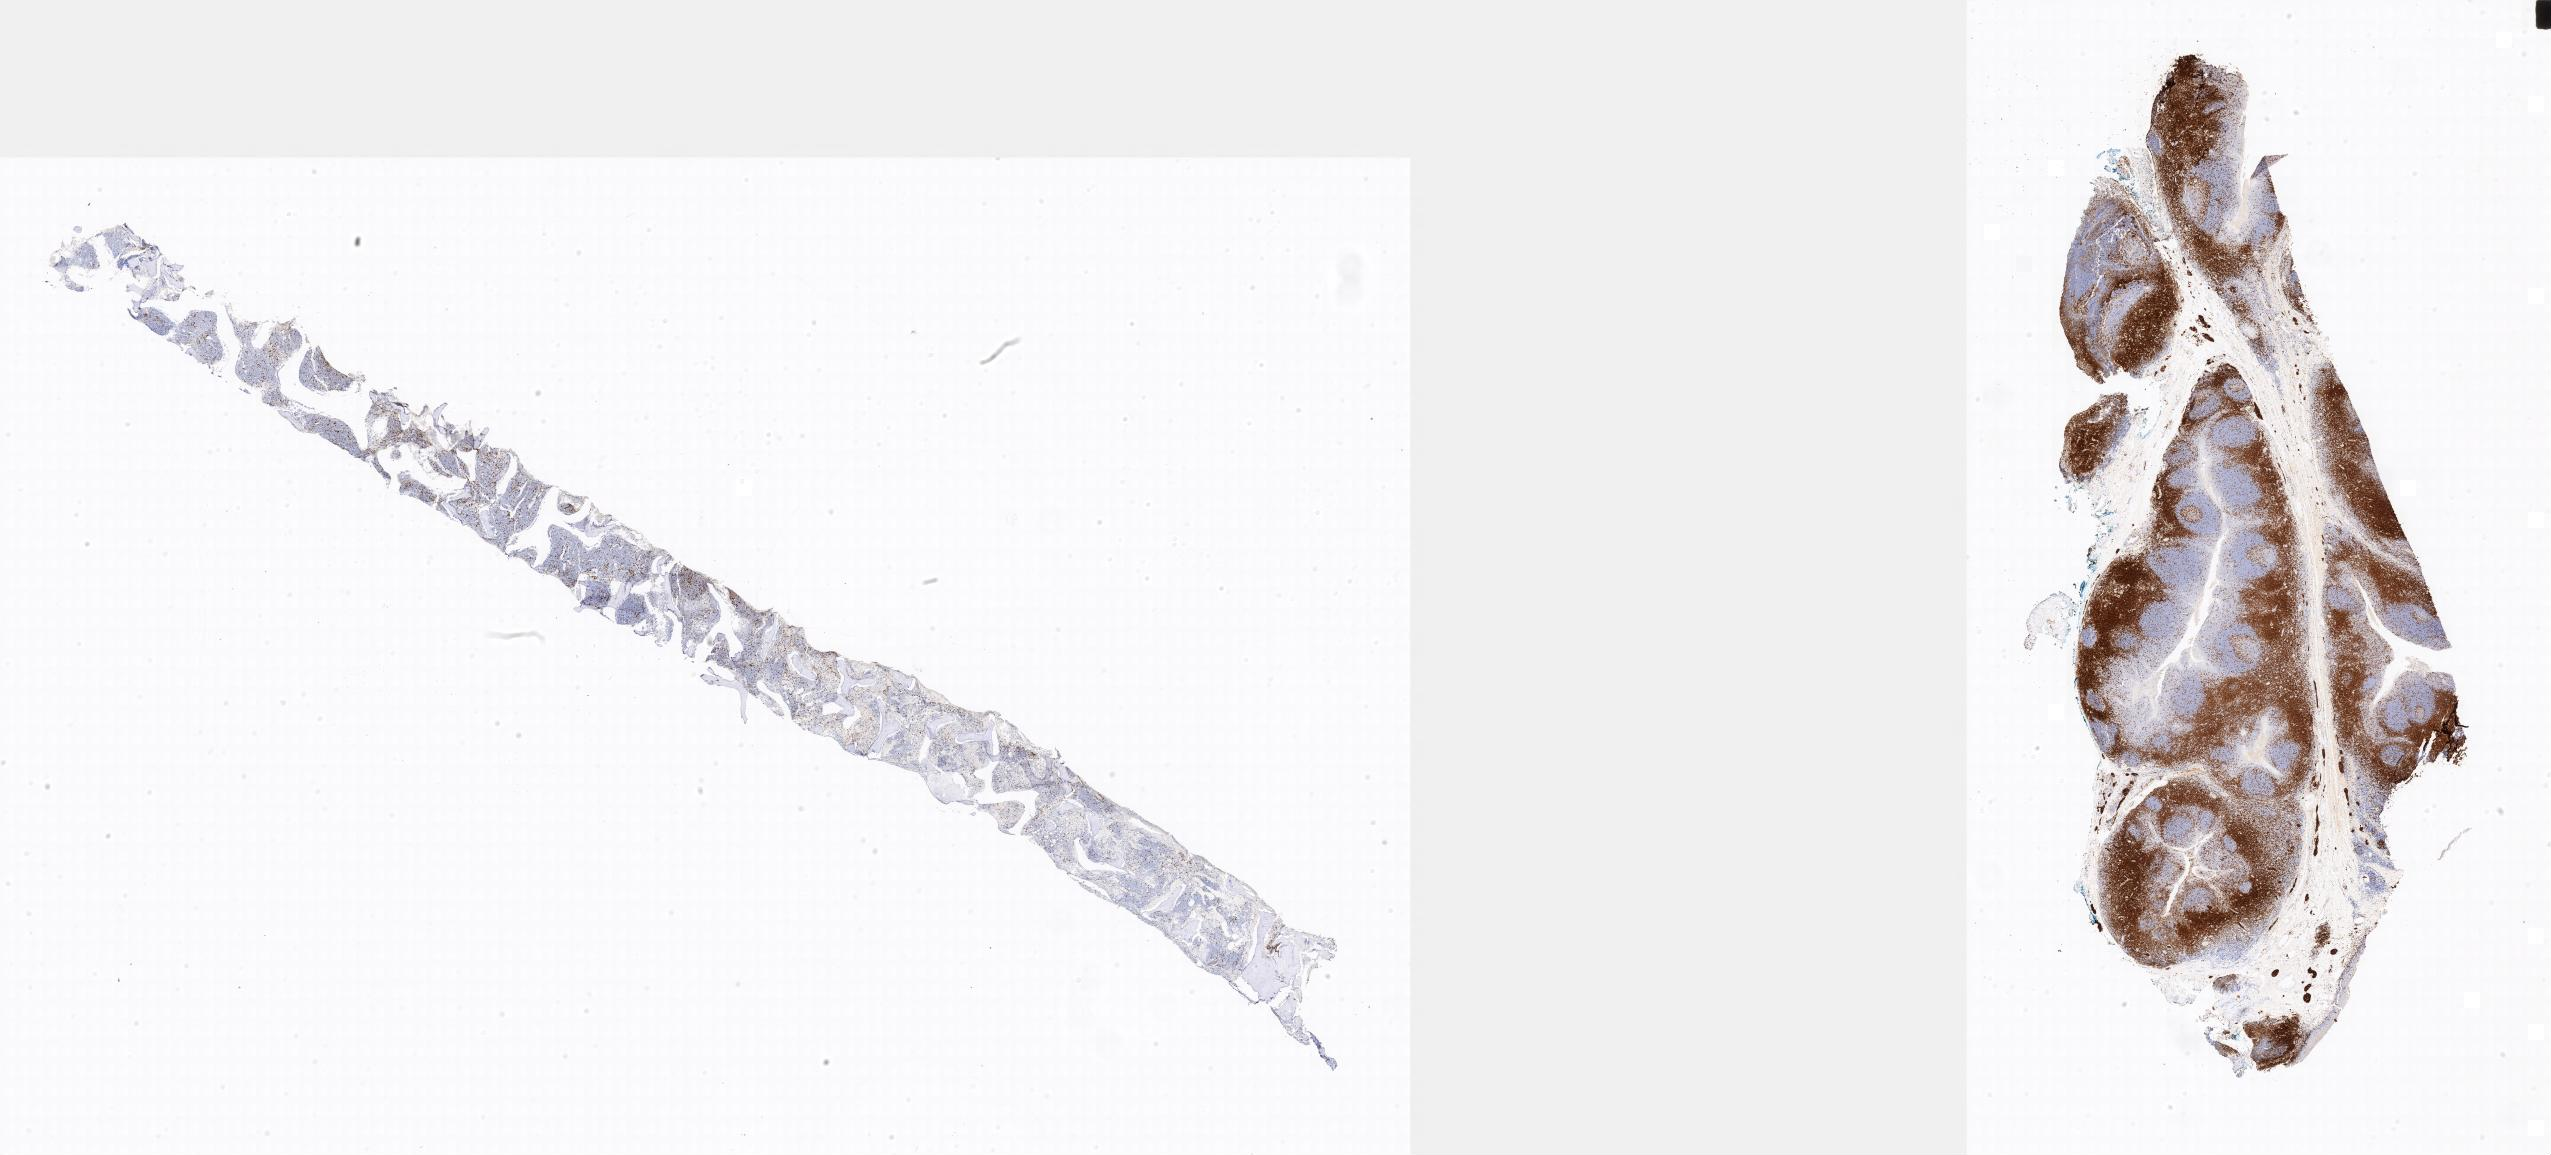
Whole-slide image, immunohistochemical stain for CD3, low-resolution overview of the scanned area. Tumor tissue. Anatomic site: bone marrow. Male patient, age 18 years.
Diagnosis: Burkitt lymphoma, NOS.